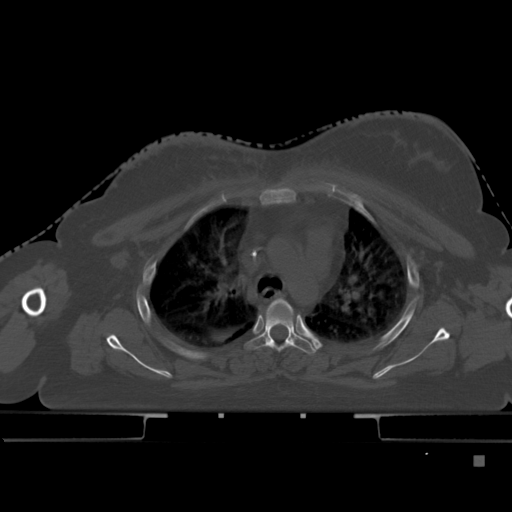
CT including the spine, one axial slice; slice 336 of 495 in the series (ordered by position); bone window (W 1800 / L 400 HU); 1.5 mm slice thickness; 512 × 512 image matrix. Patient: female, 33 years. Case-level facts recorded for this patient, not image findings: primary cancer: breast; vertebrae with lytic lesions (as recorded): T1.
Outlined on this slice (semi-automatically segmented with operator editing):
- T4 vertebra: bounding box (x1, y1, x2, y2) in pixels: (249, 299, 320, 354)